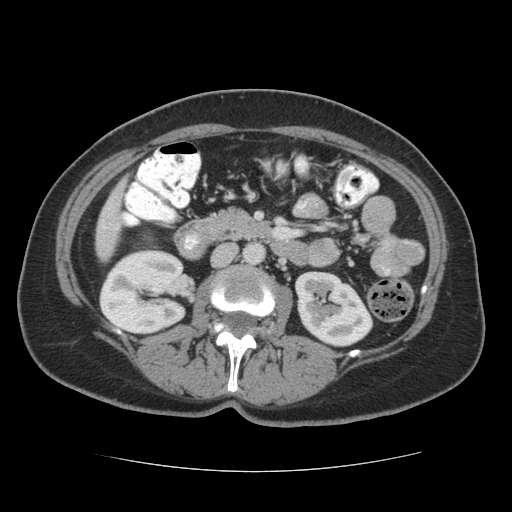
Contrast-enhanced abdominal CT (liver protocol), one axial slice. Position 12 of 75 along the scan axis. Reconstruction kernel STANDARD. 140 kVp. Soft-tissue window (W 400 / L 40 HU). 512 × 512 image matrix, field of view 360 × 360 mm. Case-level facts recorded for this patient, not image findings: diagnosis: hepatocellular carcinoma (patient treated with transarterial chemoembolisation; whether this scan precedes or follows treatment is not stated here); TNM stage (as recorded): Stage-I; Child-Pugh class: A; tumour nodularity: uninodular.
Annotated regions visible in this slice (semi-automatically segmented with operator editing):
- liver parenchyma outside the tumour (the mass and vessels are separate outlines, so this box may not span the whole liver): bounding box [x1, y1, x2, y2] px = [96, 184, 124, 259]
- liver vessels: [102, 207, 117, 229]